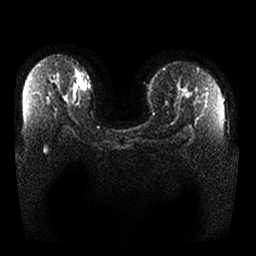
Breast MRI, one axial slice. Slice 20 of 25 in the series (ordered by position). Diffusion-weighted series; image 2 of 4 stored at this slice position (different b-values; order by instance number). 1.5 T. 256 × 256 image matrix. Female patient.
Annotated regions visible in this slice (manually delineated by an expert):
- tumour on diffusion-weighted imaging: bounding box [x1, y1, x2, y2] px = [79, 81, 86, 89]